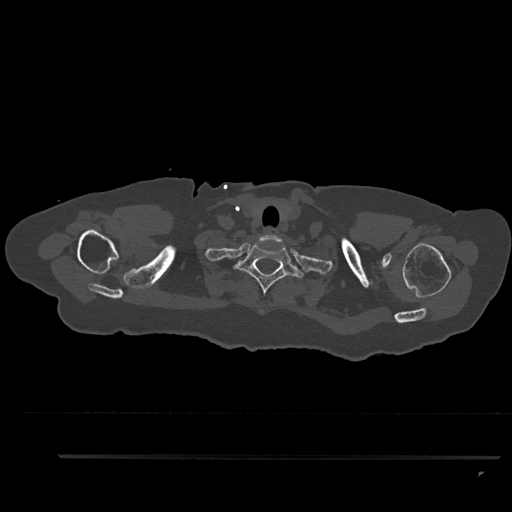
CT including the spine, one axial slice. Position 764 of 797 along the scan axis. Reconstruction kernel Br40s/3. Bone window (W 1800 / L 400 HU). 0.5 mm slice thickness. 512 × 512 image matrix, field of view 408 × 408 mm. Female patient, age 44 years. From the clinical record (not read from this slice): primary cancer: renal.
Outlined on this slice (semi-automatically segmented with operator editing):
- T1 vertebra: box from (x=233, y=245) to (x=306, y=295) px